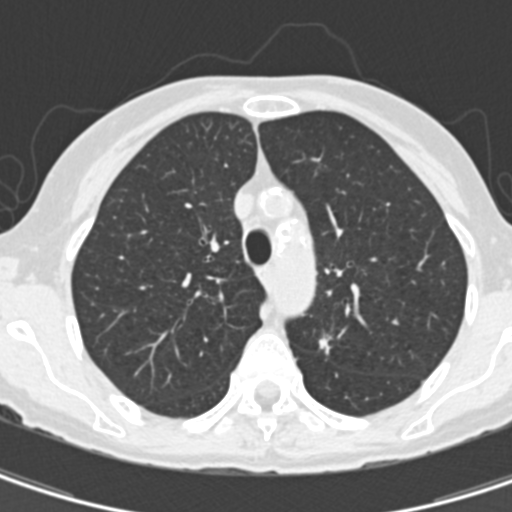
Low-dose screening chest CT, one axial slice. Reconstruction kernel B30f. 120 kVp. Lung window (W 1500 / L -600 HU). 512 × 512 image matrix, field of view 260 × 260 mm.
Outlined on this slice (outlined manually by an expert reader):
- lesion 1 (tumor, upper lobe of left lung): box from (x=319, y=335) to (x=332, y=355) px